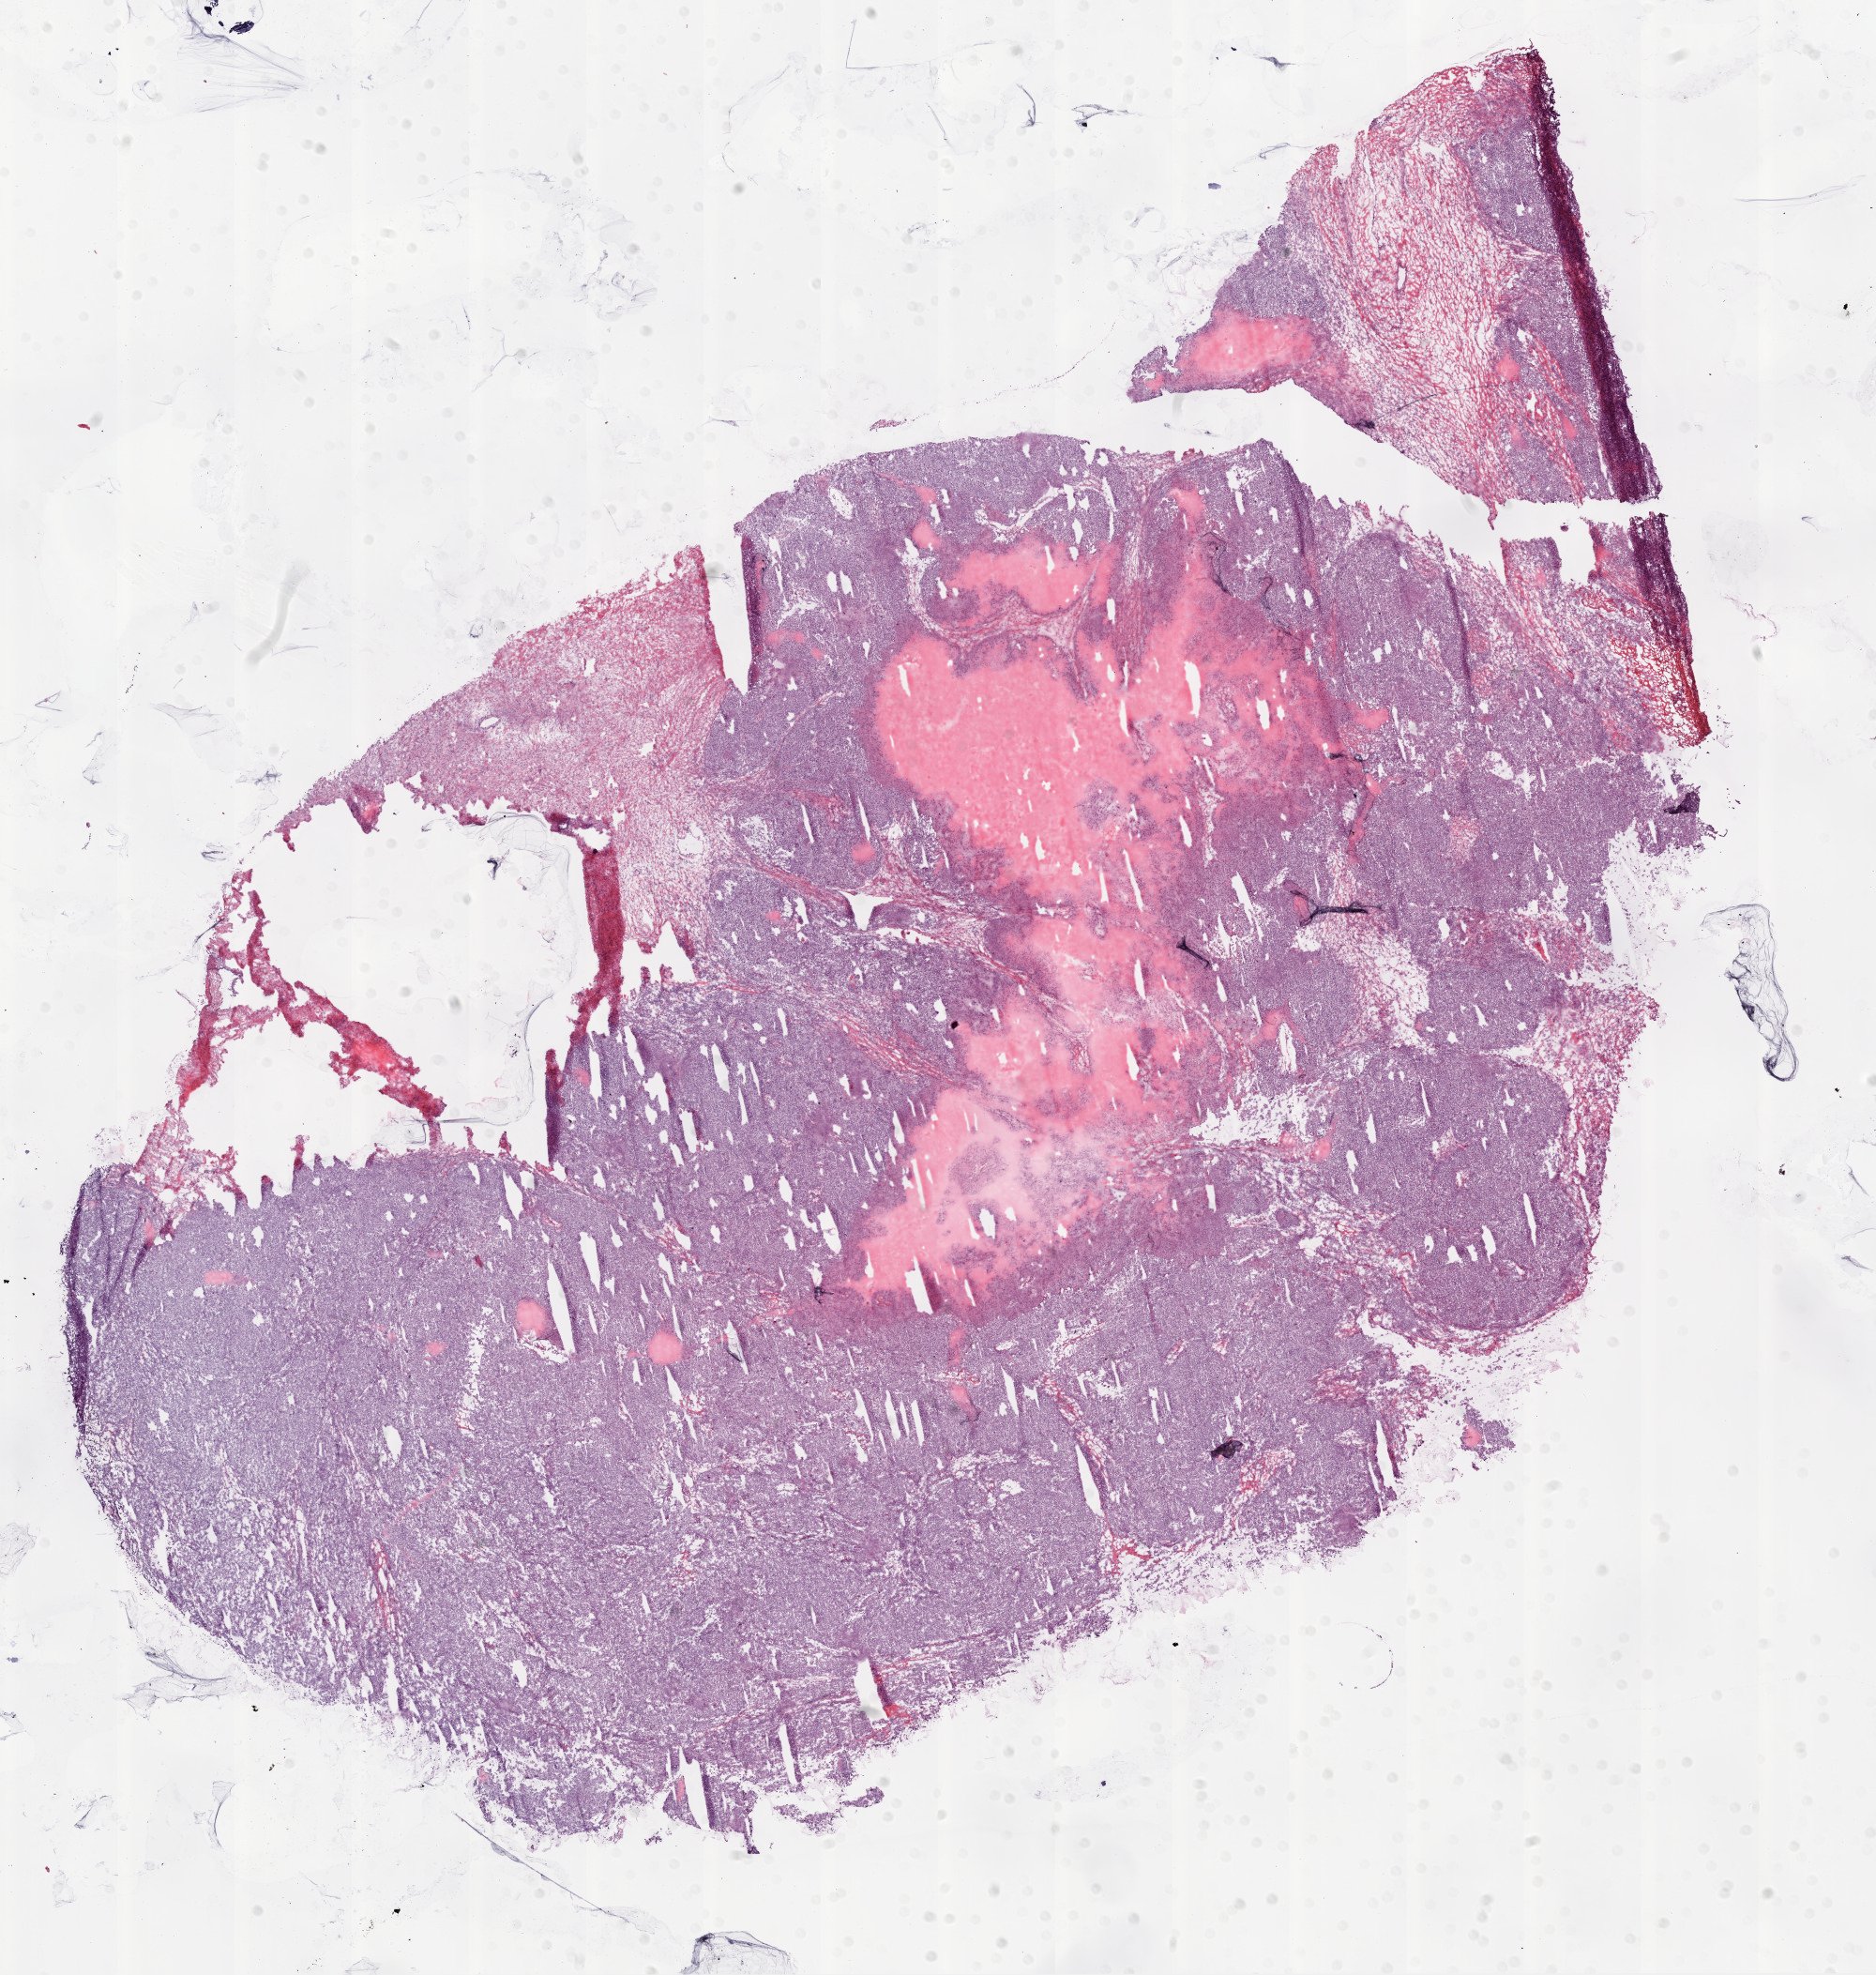
Digitized H&E-stained tissue section (whole slide), a low-resolution overview of the entire scanned area, about 16.0 x 16.9 mm; frozen section; primary tumour sample from the ovary. Patient: female, age at initial diagnosis 63 years. Histologic grade: G3 (poorly differentiated). Slide review estimates, as recorded: tumour cells 90%, tumour nuclei 99%, normal cells 0%, stromal cells 5%, necrosis 5%.
Histologic diagnosis: Serous cystadenocarcinoma, NOS. FIGO stage: IIIC. Laterality: bilateral.